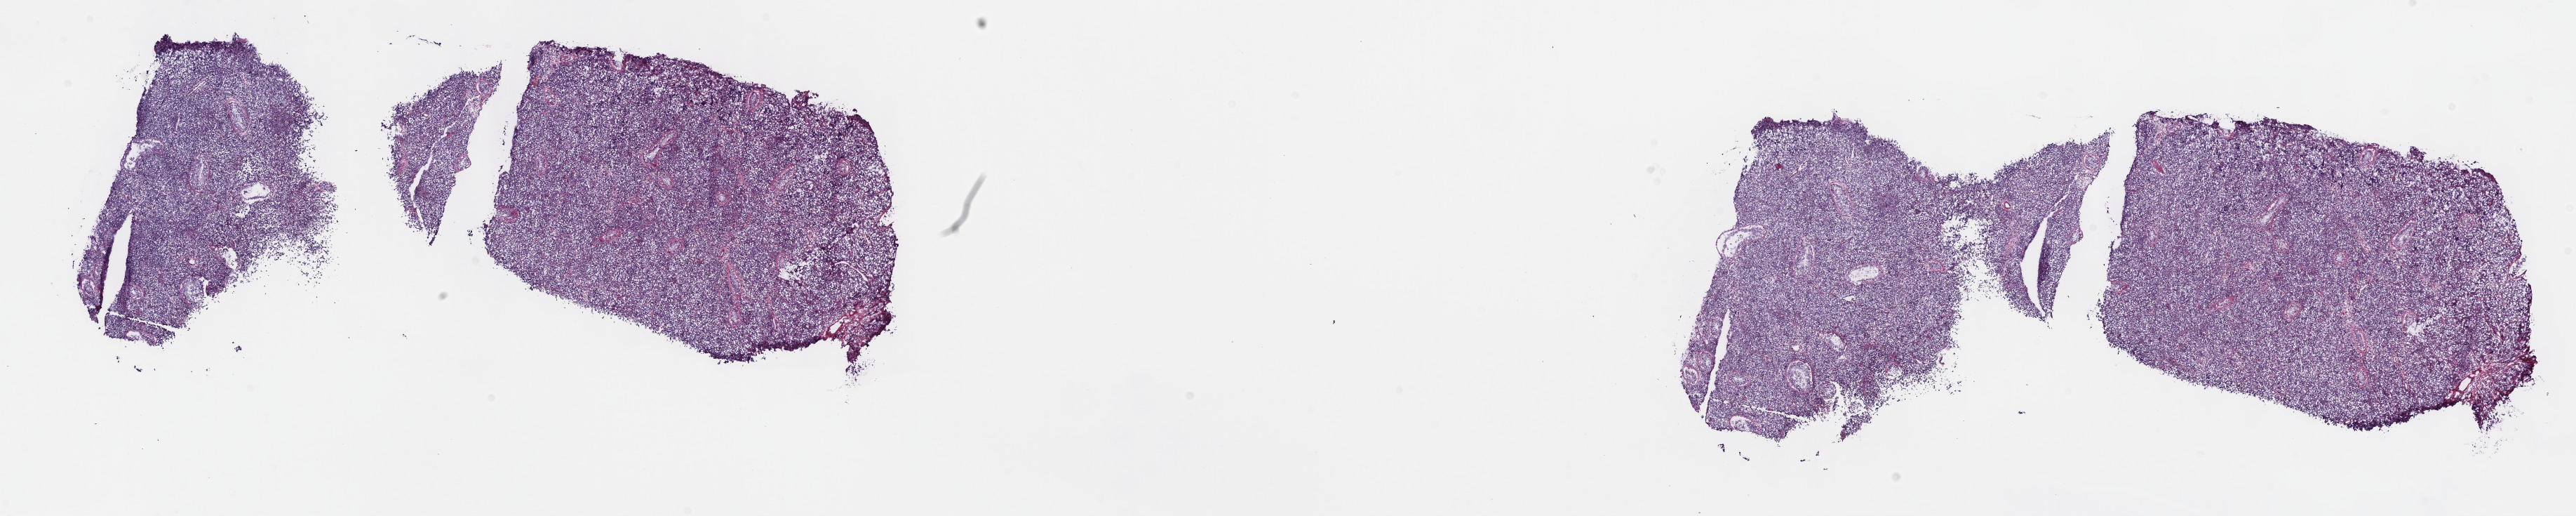
H&E-stained whole-slide image — whole scanned area (about 29.7 x 5.9 mm, slide scanned at 40x) shown as a low-resolution overview. Frozen section from the top of the tissue portion. Primary tumour sample from the testis. Patient: male, age at initial diagnosis 37 years. Composition of this section per pathologist review: tumour cells 100%, tumour nuclei 75%, normal cells 0%, stromal cells 0%, necrosis 0%. Infiltration values recorded for this section: lymphocyte infiltration 2%, monocyte infiltration 0%, neutrophil infiltration 0%.
- diagnosis: Seminoma, NOS
- laterality: bilateral
- TNM: T2 N1 M0
- AJCC pathologic stage: IIA